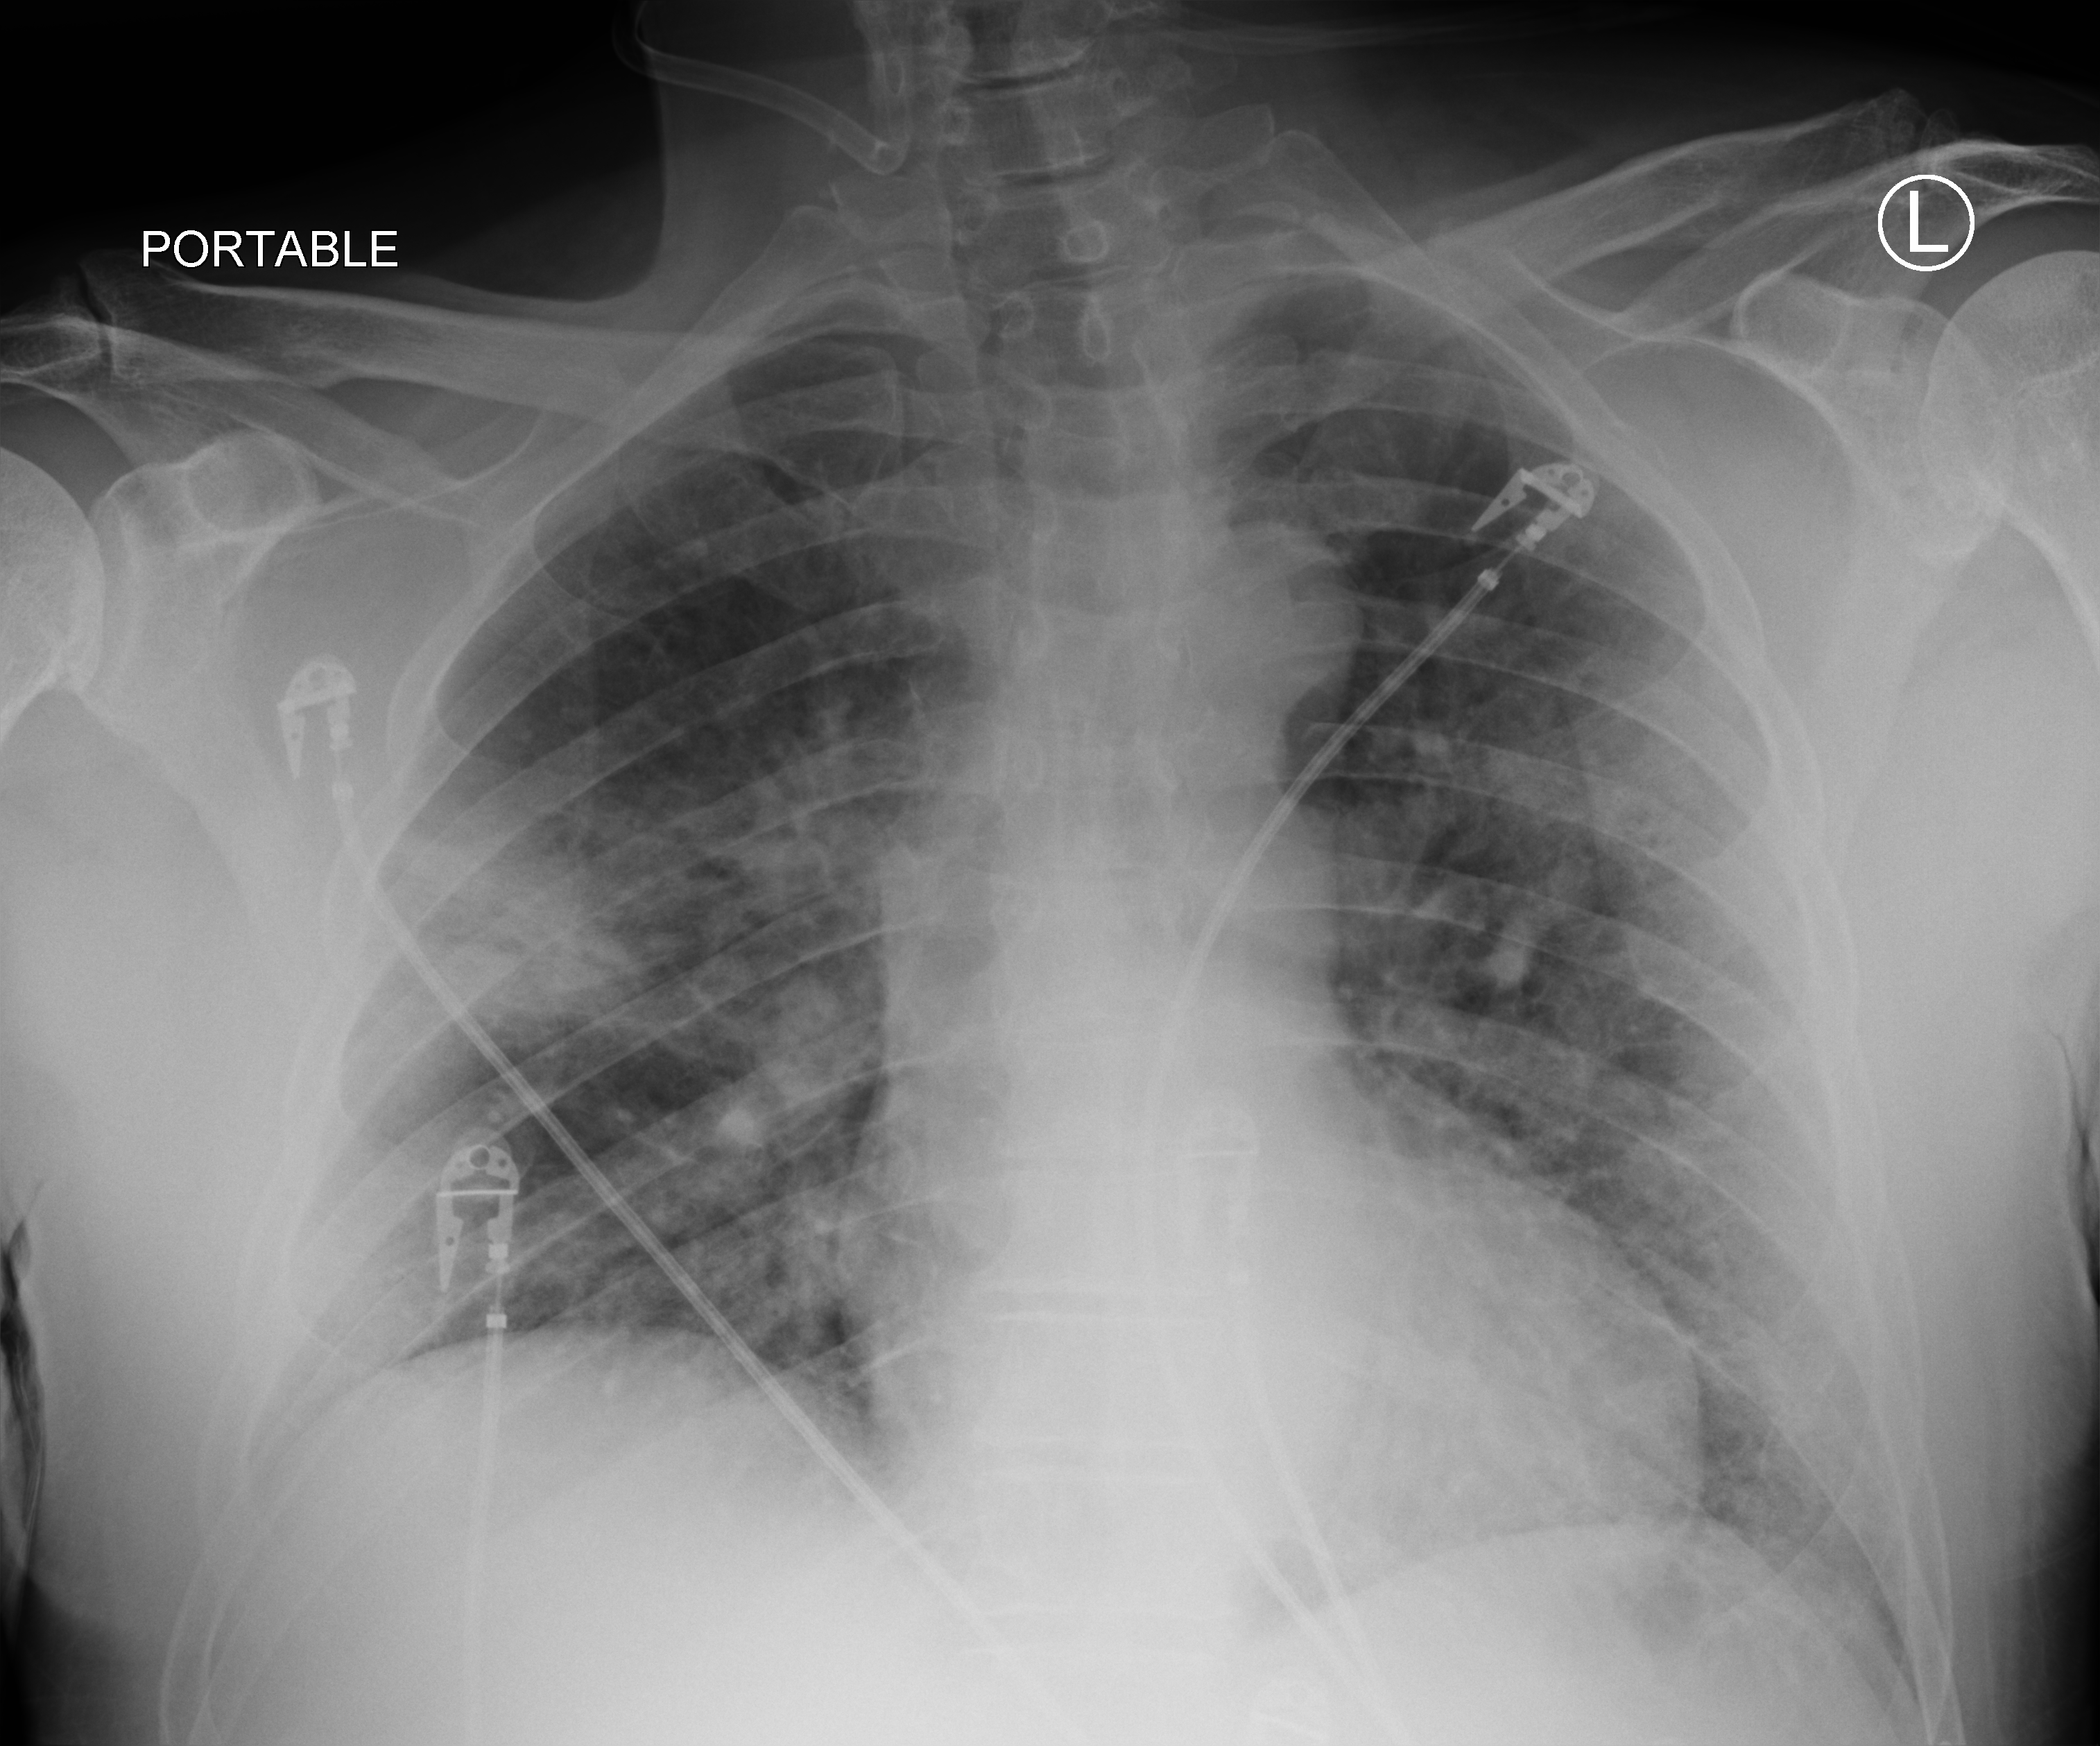
Portable chest radiograph. Patient hospitalised with COVID-19; male, aged 18–59 years.
Hospital-stay facts (about this admission, not read from this image; timing relative to this image not recorded): mechanically ventilated during this hospital stay: no; admitted to intensive care during this hospital stay: no.